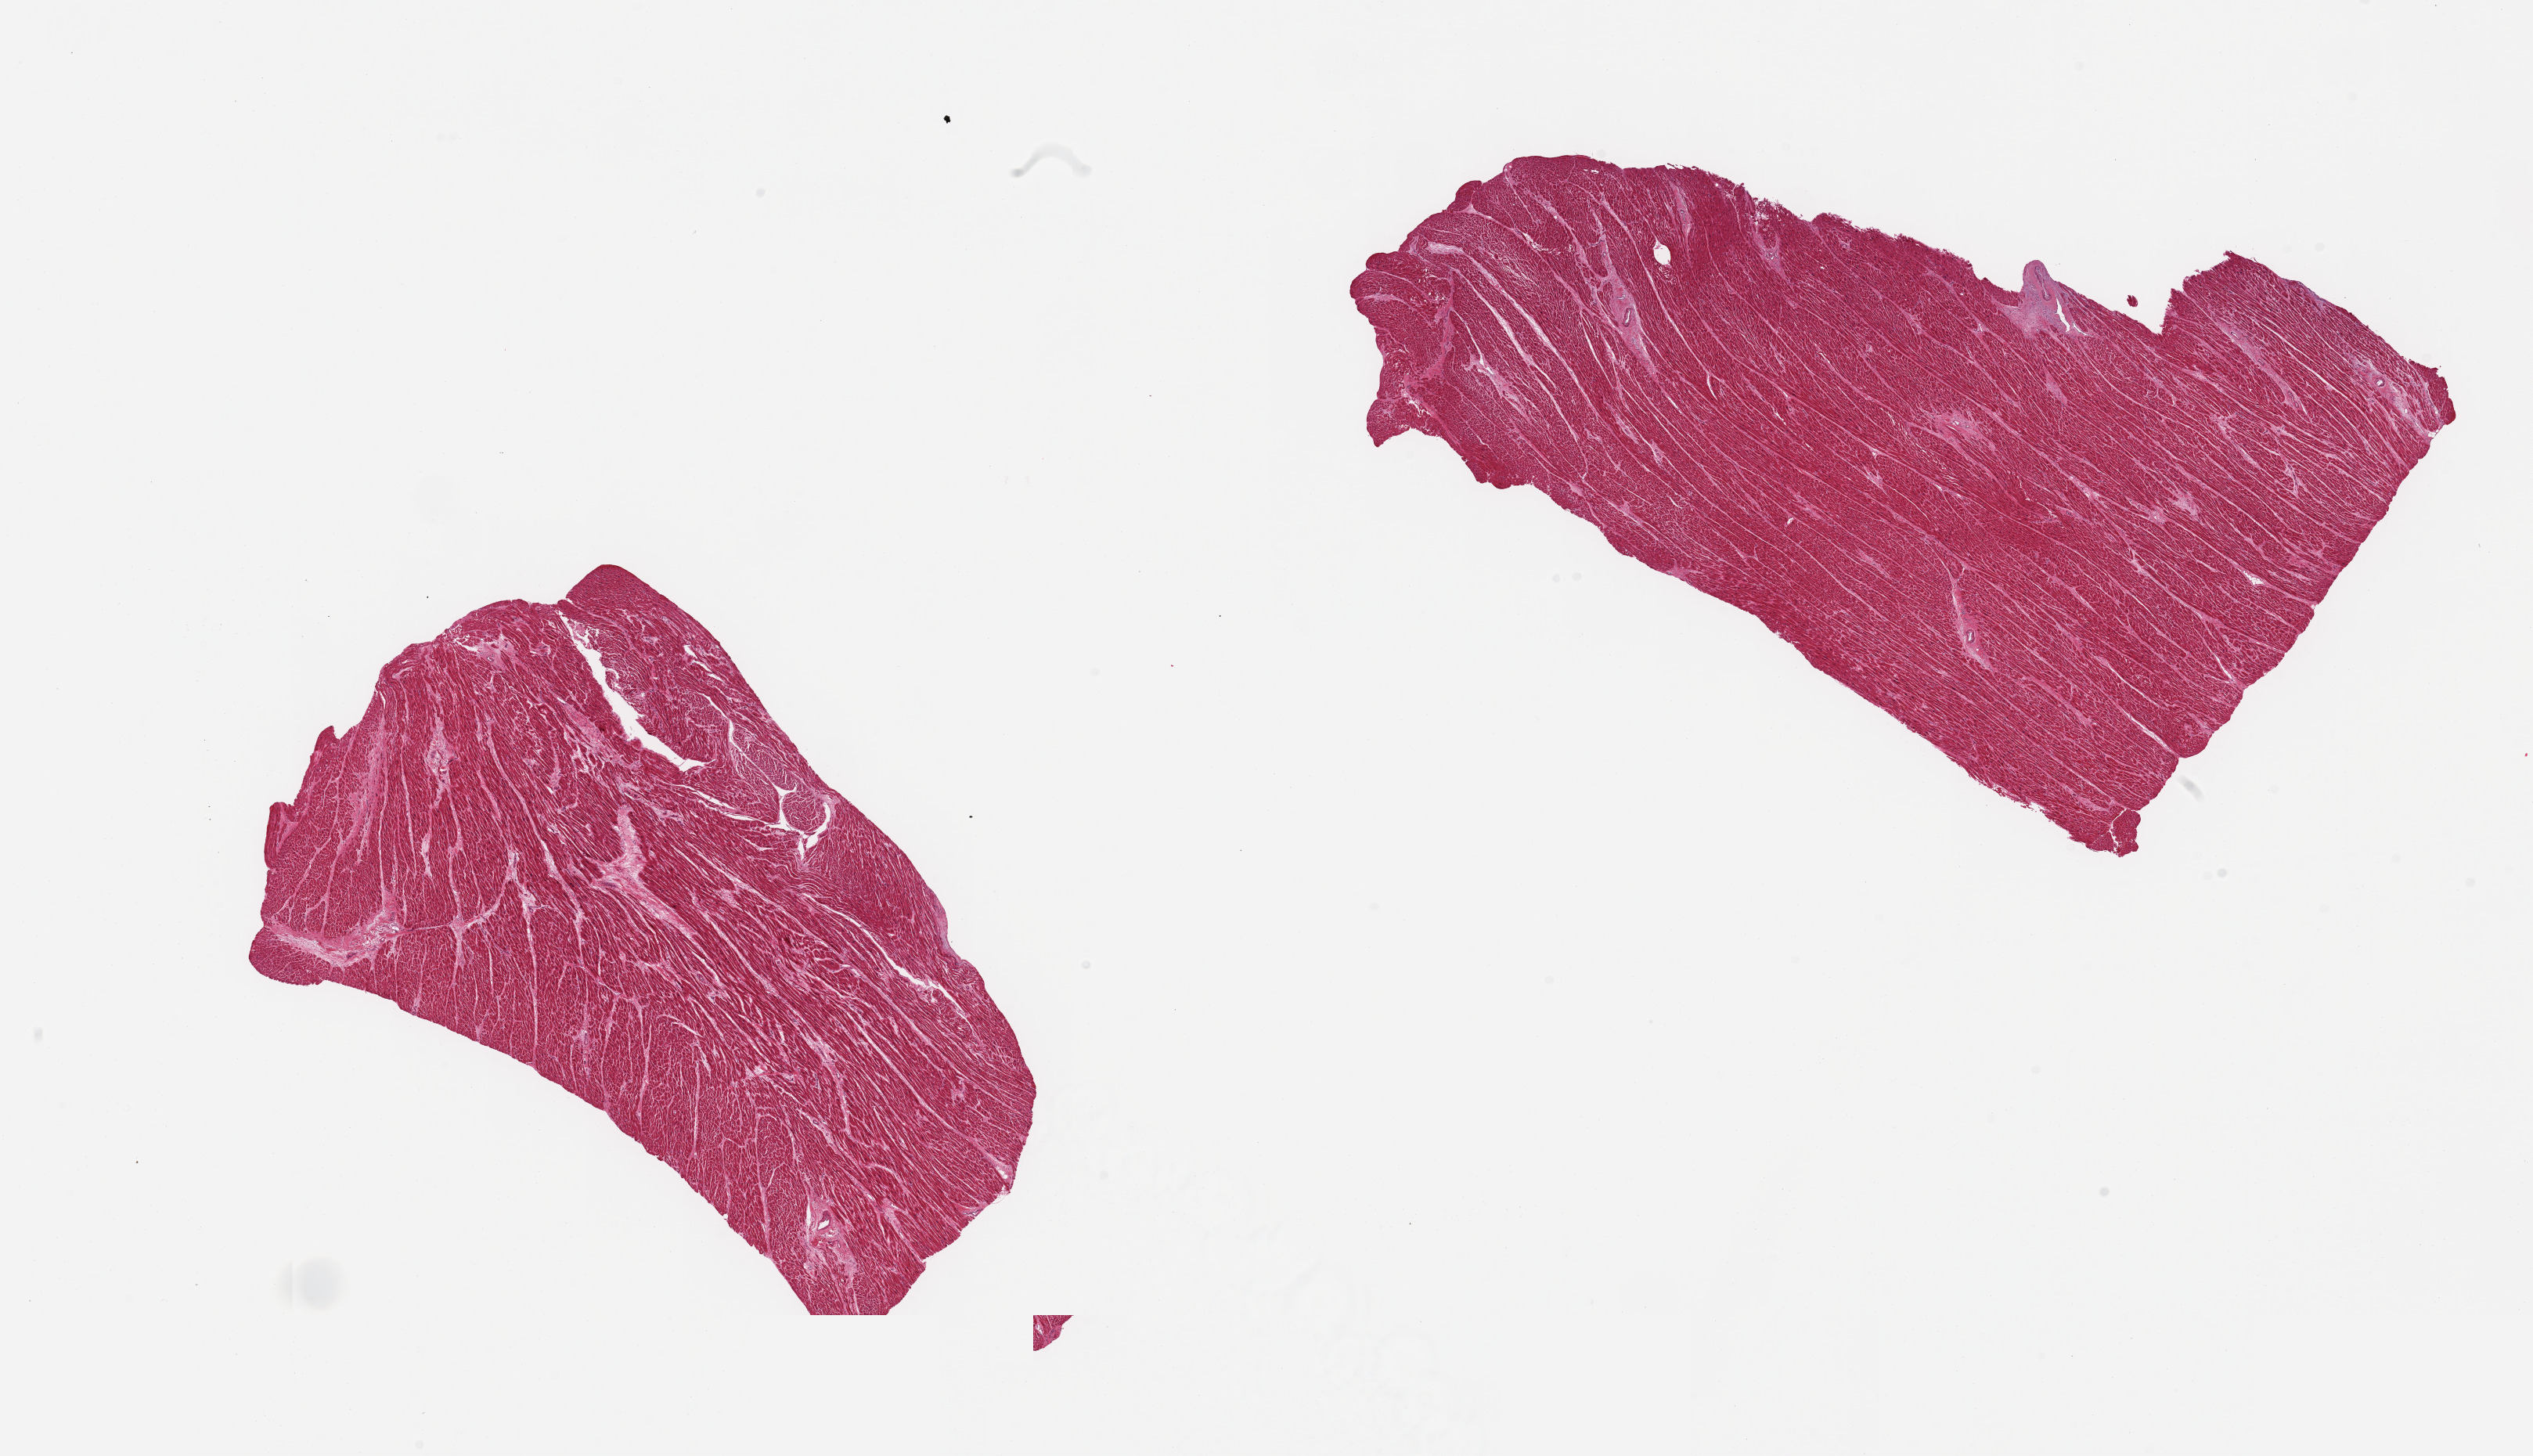
Haematoxylin and eosin whole-slide image, brightfield — a low-resolution overview of the entire scanned area, about 25.6 x 14.7 mm (from a 20x scan). PAXgene-fixed paraffin-embedded (PFPE) section. Section of heart (target tissue). Tissue donor sample. Female donor.
Review note (as recorded): 2 pieces; small foci of interstitial fibrosis.